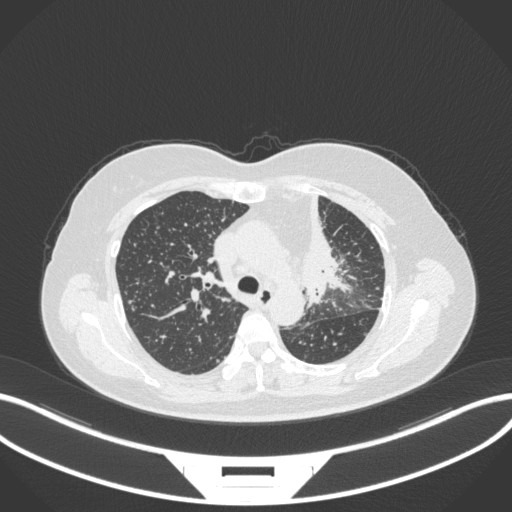
Chest CT, one axial slice. Reconstruction kernel B31f. 120 kVp. Lung window (W 1500 / L -600 HU). 1 mm slice thickness. 512 × 512 image matrix, field of view 400 × 400 mm. Patient: female, 49 years. Case-level facts recorded for this patient, not image findings: clinical TNM (as recorded): T1c N0 M1.
Annotated regions visible in this slice (bounding box drawn by a radiologist):
- lung tumour (recorded histology: adenocarcinoma): bounding box <301,196,351,307> (left, top, right, bottom; pixels)